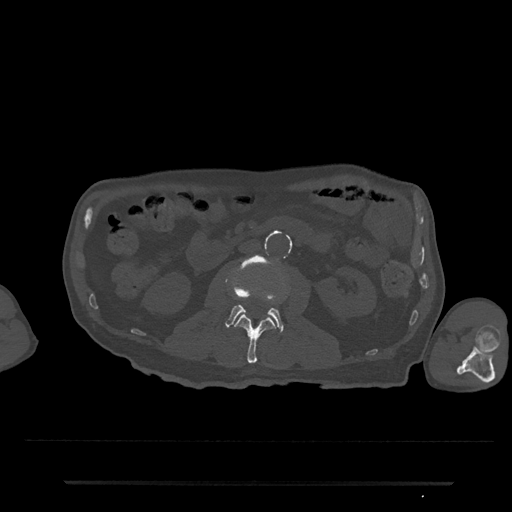
CT including the spine, one axial slice; position 26 of 797 along the scan axis; reconstruction kernel Br40s/3; 120 kVp; bone window (W 1800 / L 400 HU); 0.5 mm slice thickness; 512 × 512 image matrix, field of view 427 × 427 mm. Male patient, age 74 years. From the clinical record (not read from this slice): primary cancer: prostate.
Annotated regions visible in this slice (semi-automatic segmentation, software-assisted and operator-edited):
- L2 vertebra: bounding box (x1, y1, x2, y2) in pixels: (236, 315, 275, 364)
- L3 vertebra: (225, 256, 284, 333)